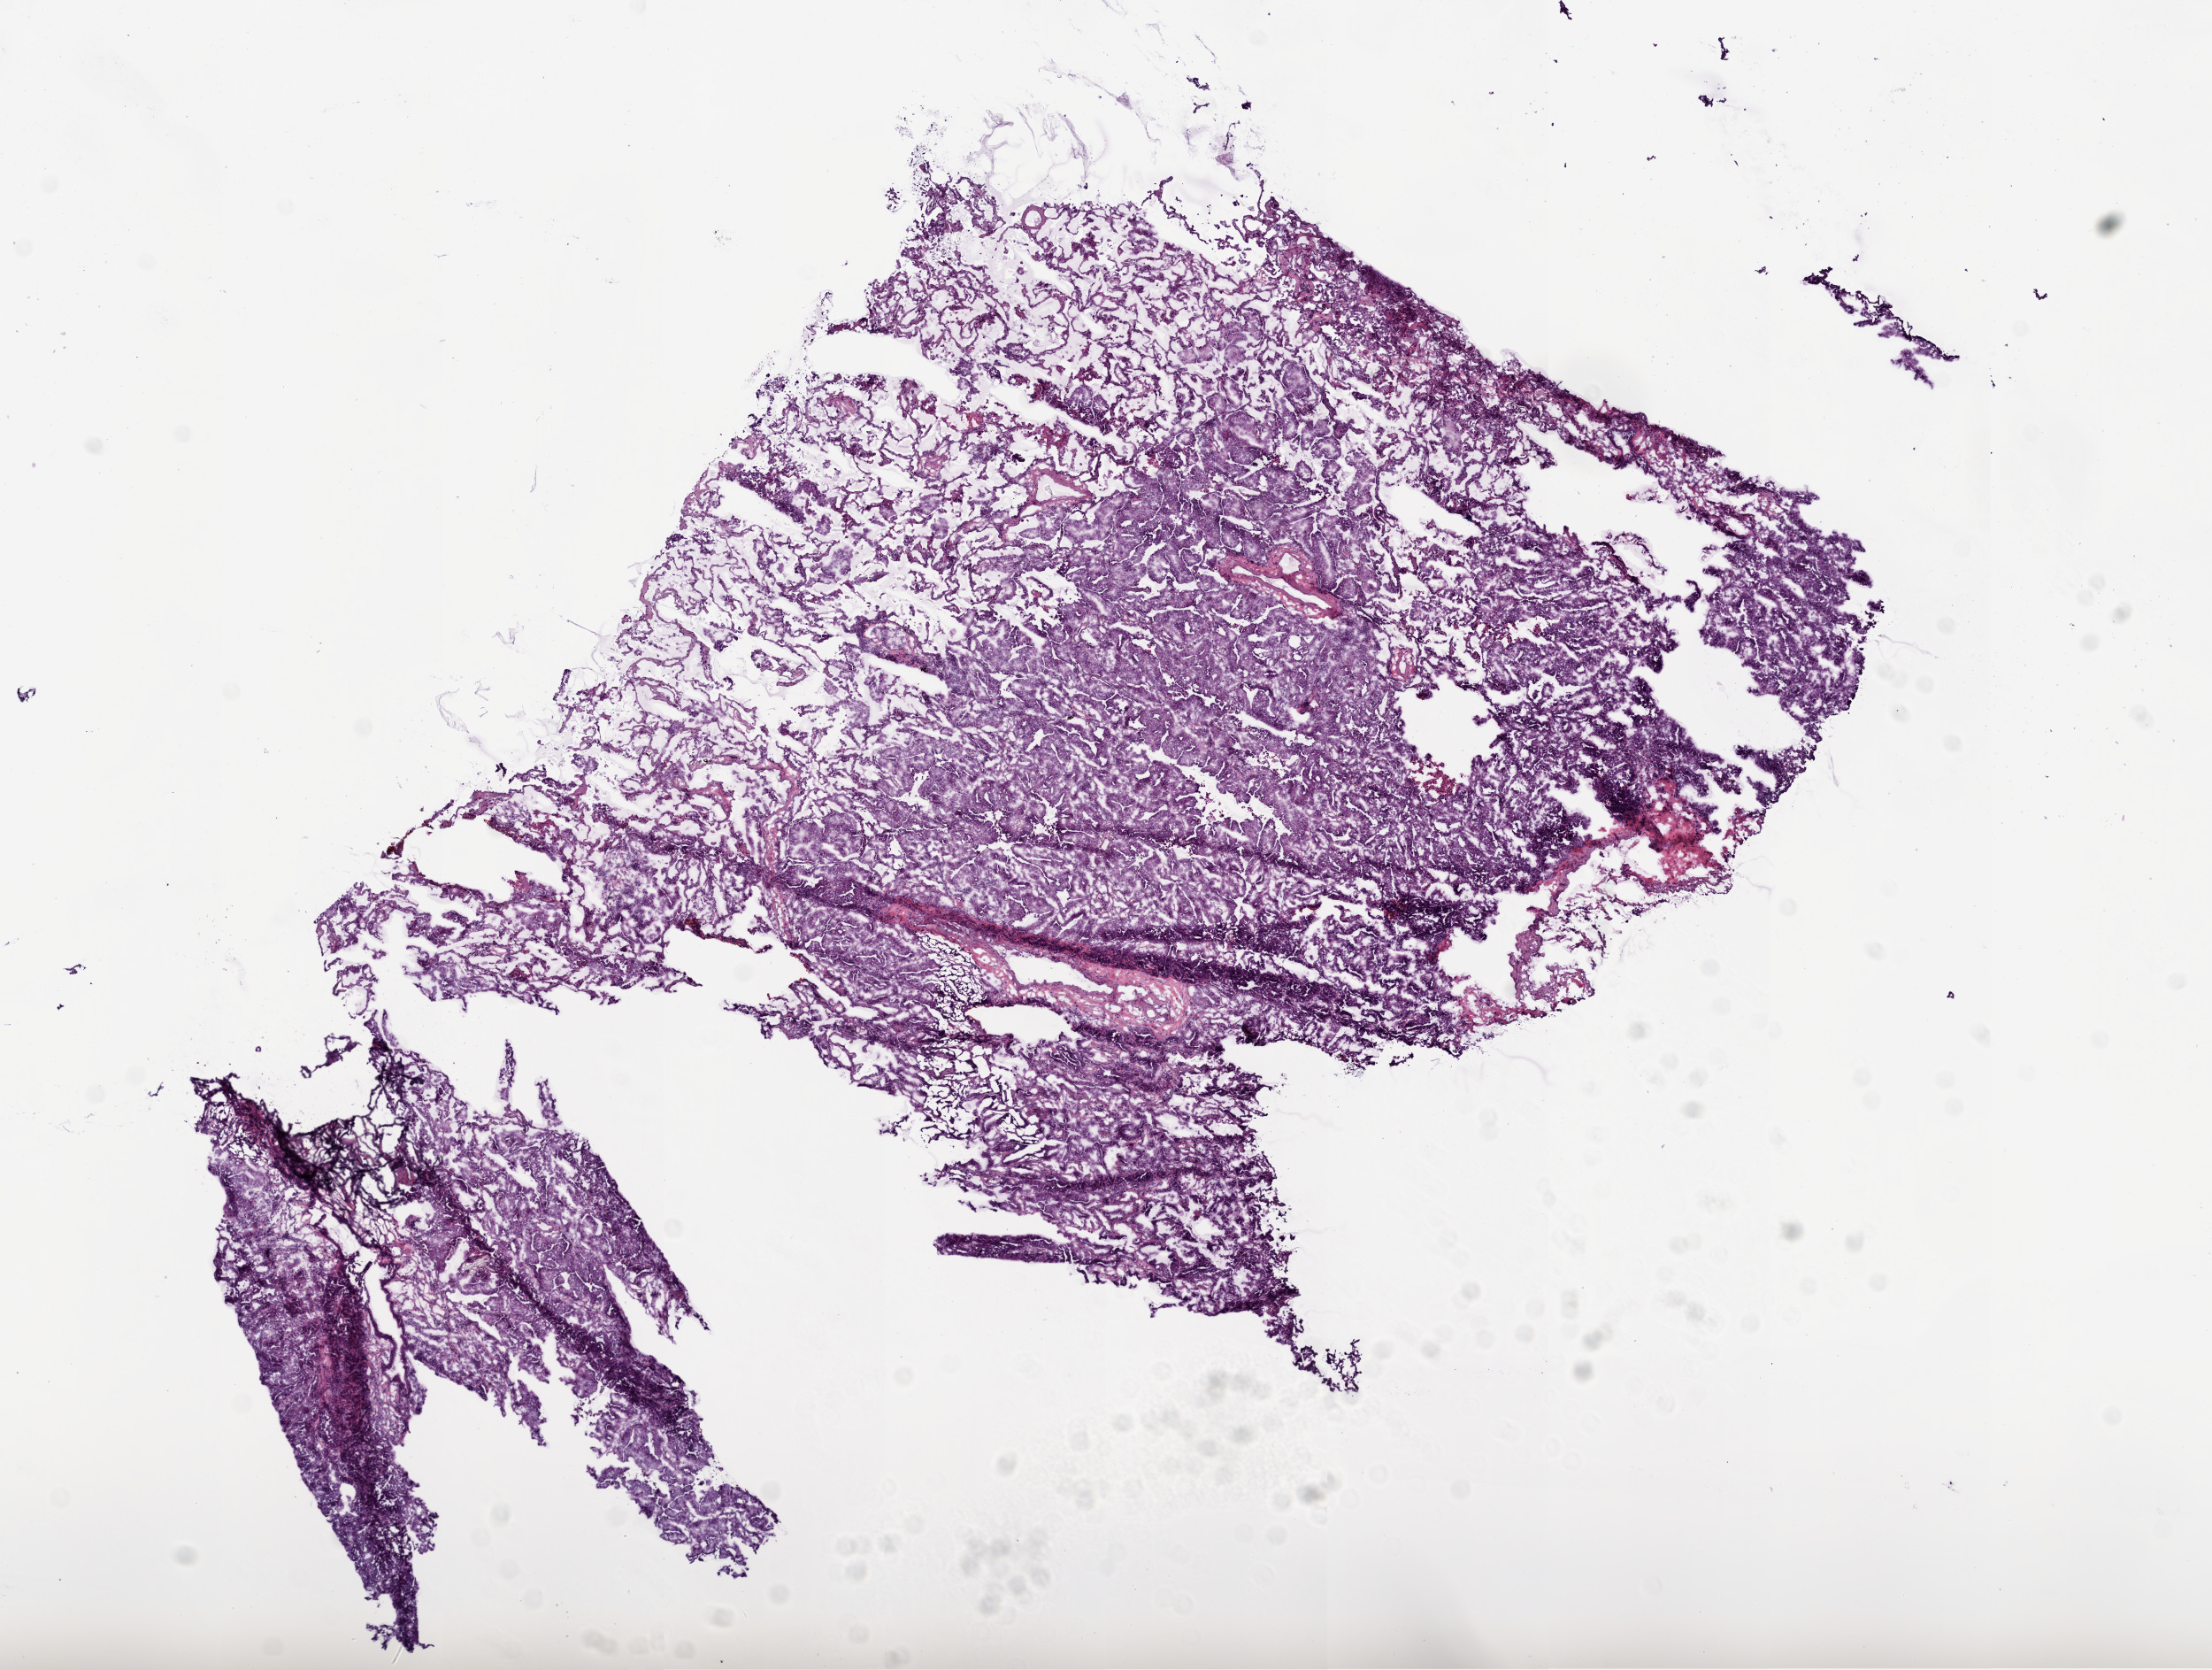
H&E whole-slide image — whole scanned area (about 10.0 x 7.6 mm) shown as a low-resolution overview. Frozen section from the top of the tissue portion. Primary tumour sample from the lung. Patient: male, age at initial diagnosis 67 years. Slide review estimates, as recorded: tumour cells 80%, tumour nuclei 80%, normal cells 19%, stromal cells 0%, necrosis 1%. Infiltration values recorded for this section: lymphocyte infiltration 2%, monocyte infiltration 5%, neutrophil infiltration 0%.
TNM: T1a N0 M0. AJCC pathologic stage: IA (7th edition). Pathologic diagnosis: Adenocarcinoma with mixed subtypes (upper lobe, lung).